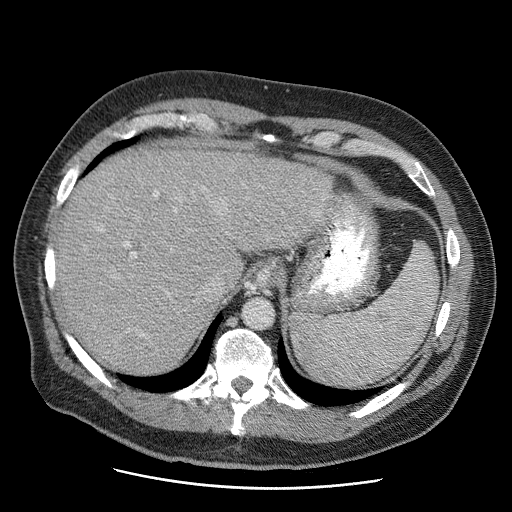
Contrast-enhanced abdominal CT (liver protocol), one axial slice; position 44 of 81 along the scan axis; reconstruction kernel STANDARD; soft-tissue window (W 400 / L 40 HU); 2.5 mm slice thickness; 512 × 512 image matrix, field of view 380 × 380 mm. Case-level facts recorded for this patient, not image findings: diagnosis: hepatocellular carcinoma (patient treated with transarterial chemoembolisation; whether this scan precedes or follows treatment is not stated here); TNM stage (as recorded): Stage-IIIA; Child-Pugh class: A; tumour differentiation: moderately differentiated; tumour size: 5.5 cm.
Annotated regions visible in this slice (semi-automatically segmented with operator editing):
- liver parenchyma outside the tumour (the mass and vessels are separate outlines, so this box may not span the whole liver): bounding box <56,148,332,374> (left, top, right, bottom; pixels)
- liver vessels: <126,194,157,256>